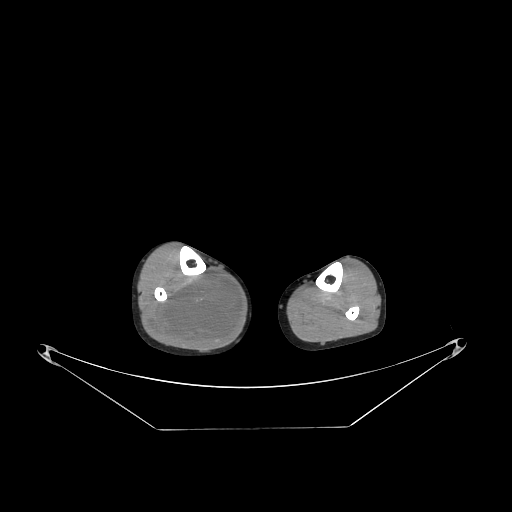
CT of an extremity soft-tissue mass (from a PET/CT study), one axial slice. Position 99 of 267 along the scan axis. 140 kVp. Soft-tissue window (W 400 / L 40 HU). 3.75 mm slice thickness. 512 × 512 image matrix, field of view 500 × 500 mm. Male patient. From the clinical record (not read from this slice): histological type: liposarcoma - round cell; grade: high; site of the primary tumour: right calf.
Annotated regions visible in this slice (expert contour drawn on MRI and transferred to this co-registered scan by the dataset authors):
- gross tumour volume (mass): box from (x=153, y=270) to (x=241, y=348) px